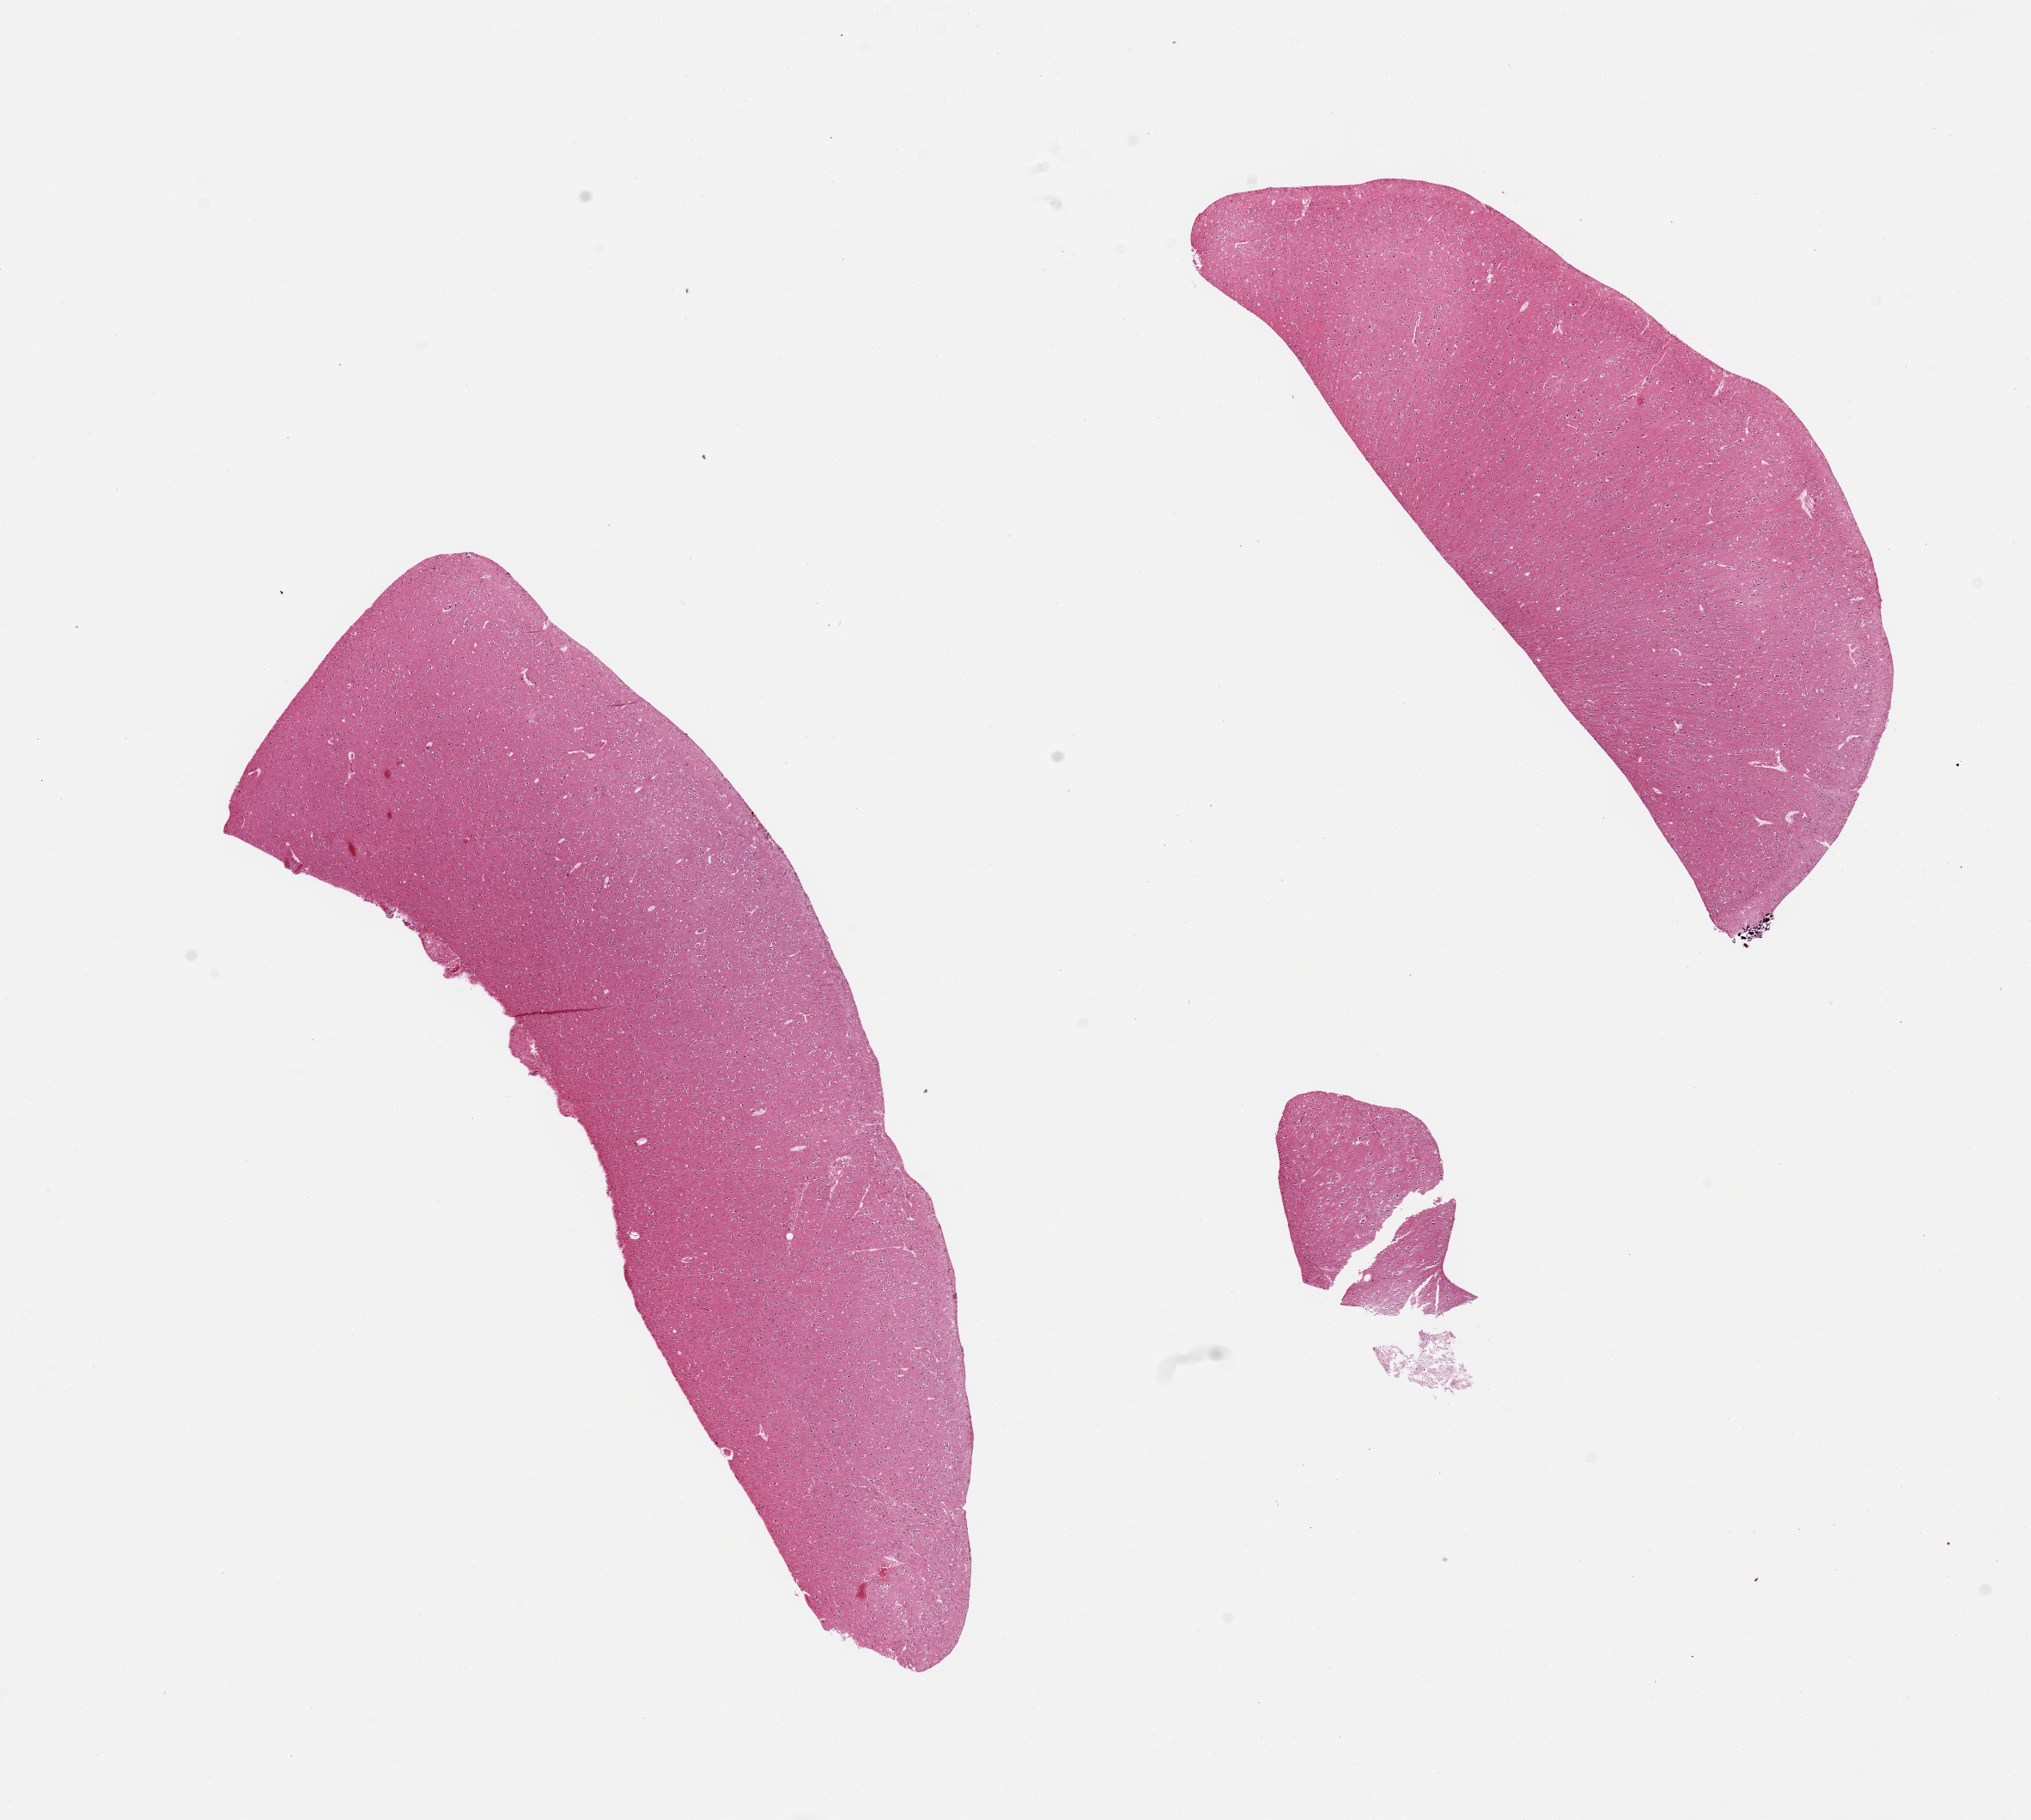
Hematoxylin and eosin (H&E) whole-slide image — low-resolution overview of the scanned area, about 18.7 x 16.8 mm (slide scanned at 20x); PAXgene-fixed, paraffin-embedded tissue; target tissue: cerebral cortex; tissue donor sample. Donor: male.
Pathologist's review note for this sample: 2 pieces, no histologic abnormality.